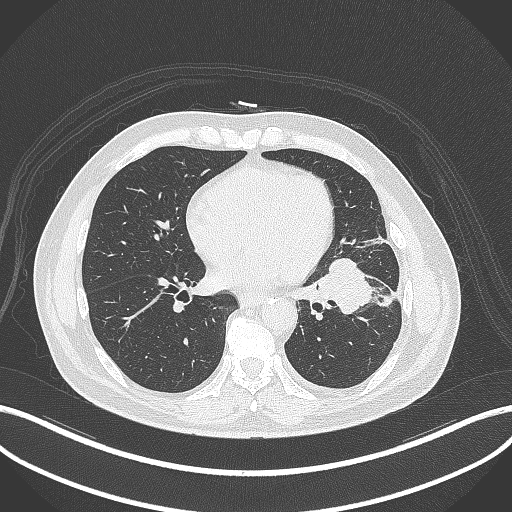
Chest CT, one axial slice. Position 150 of 230 along the scan axis. Reconstruction kernel B70f. Lung window (W 1500 / L -600 HU). 1 mm slice thickness. 512 × 512 image matrix. Patient: male, 68 years. From the clinical record (not read from this slice): clinical TNM (as recorded): T2b N0 M0.
Annotated regions visible in this slice (bounding box drawn by a radiologist):
- lung tumour (recorded histology: squamous cell carcinoma): bounding box [x1, y1, x2, y2] px = [310, 254, 376, 315]